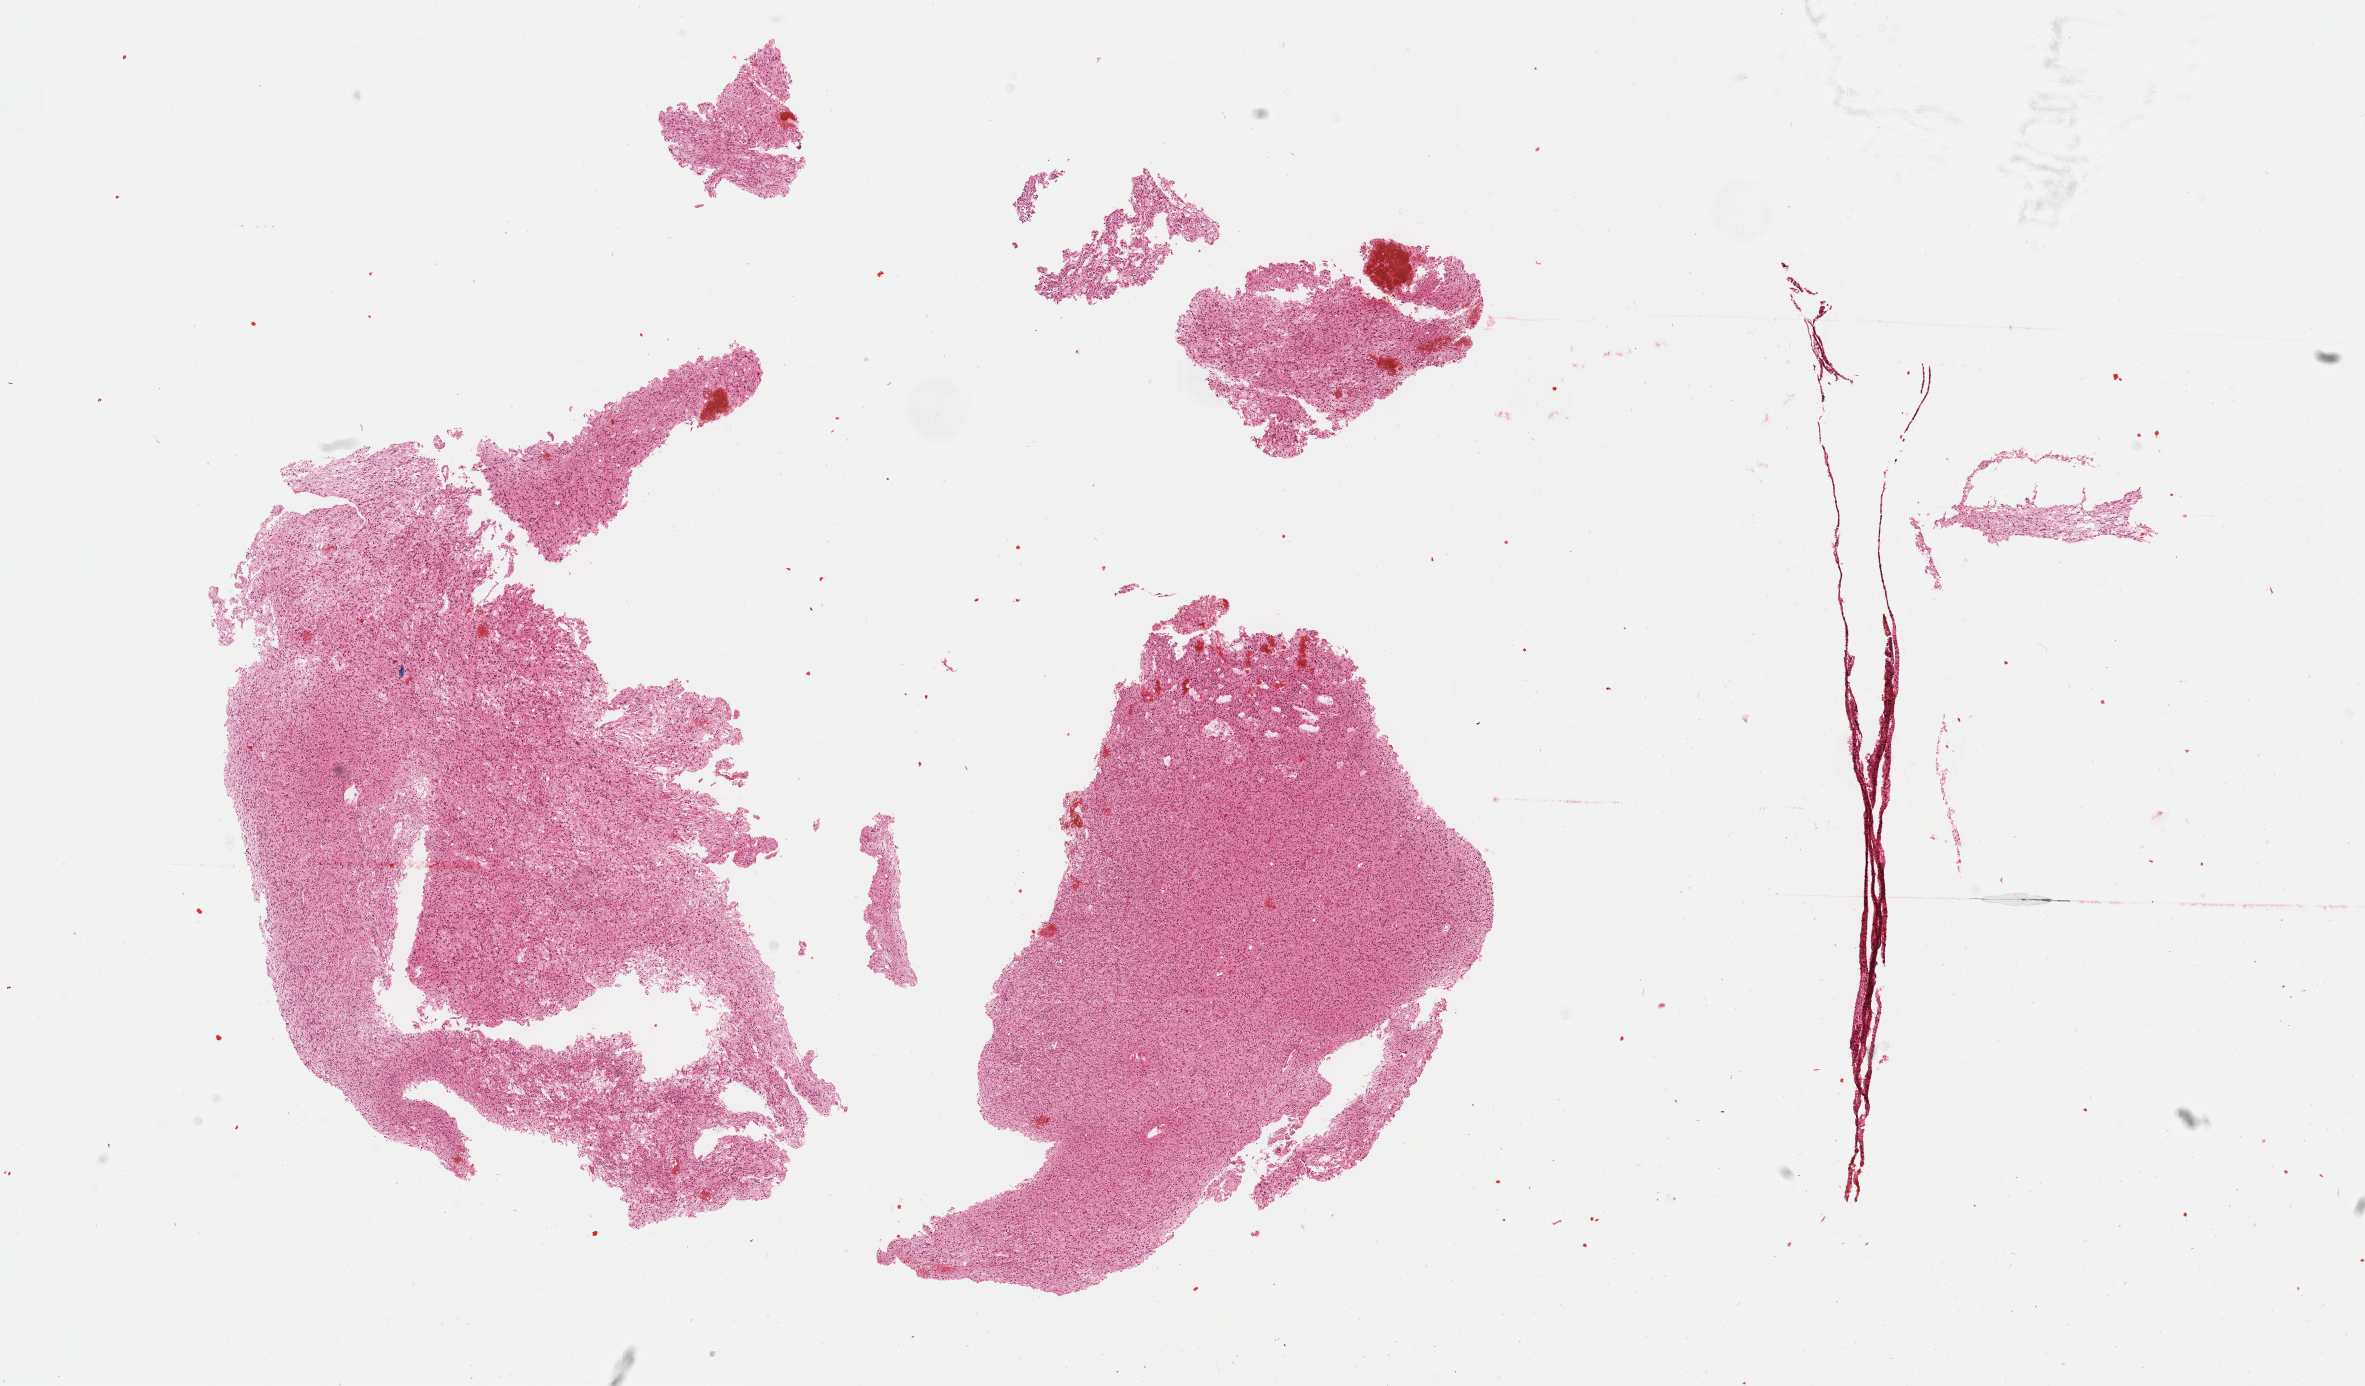
Digitized H&E tissue section (whole slide) — shown as a low-resolution overview of the whole scanned area (about 19.1 x 11.2 mm). Formalin-fixed paraffin-embedded (FFPE) diagnostic section. Primary tumour sample from the brain. Patient: female, age at initial diagnosis 54 years. Histologic grade: G3 (poorly differentiated).
Diagnosis: Astrocytoma, anaplastic.